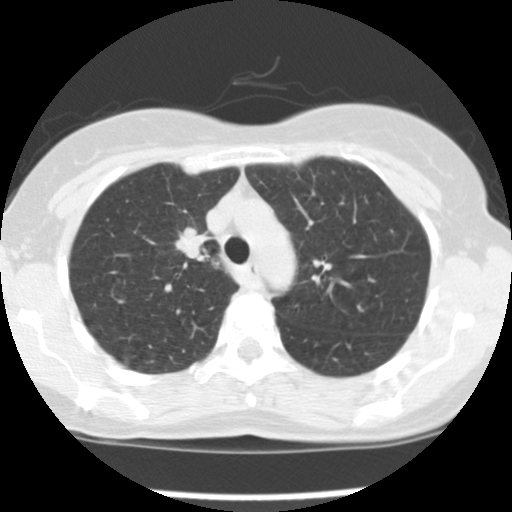
Axial slice from a low-dose chest CT screening exam. Baseline screening round. Lung window (W 1500 / L -600 HU). 512 × 512 image matrix, field of view 282 × 282 mm. Female, age 57 years at enrolment.
• Expert-annotated lung lesion, bounding box (x1, y1, x2, y2) in pixels: (166, 227, 217, 272).
• The exam's reader record, not a measurement of the box and not confirmed to be the same lesion: non-calcified nodule or mass ≥4 mm, left upper lobe, 7 × 6 mm, poorly defined margins, ground glass attenuation.
• Note: the box lies in the patient's right hemithorax on this image, whereas the reader's record names the left lung; they may be different findings.